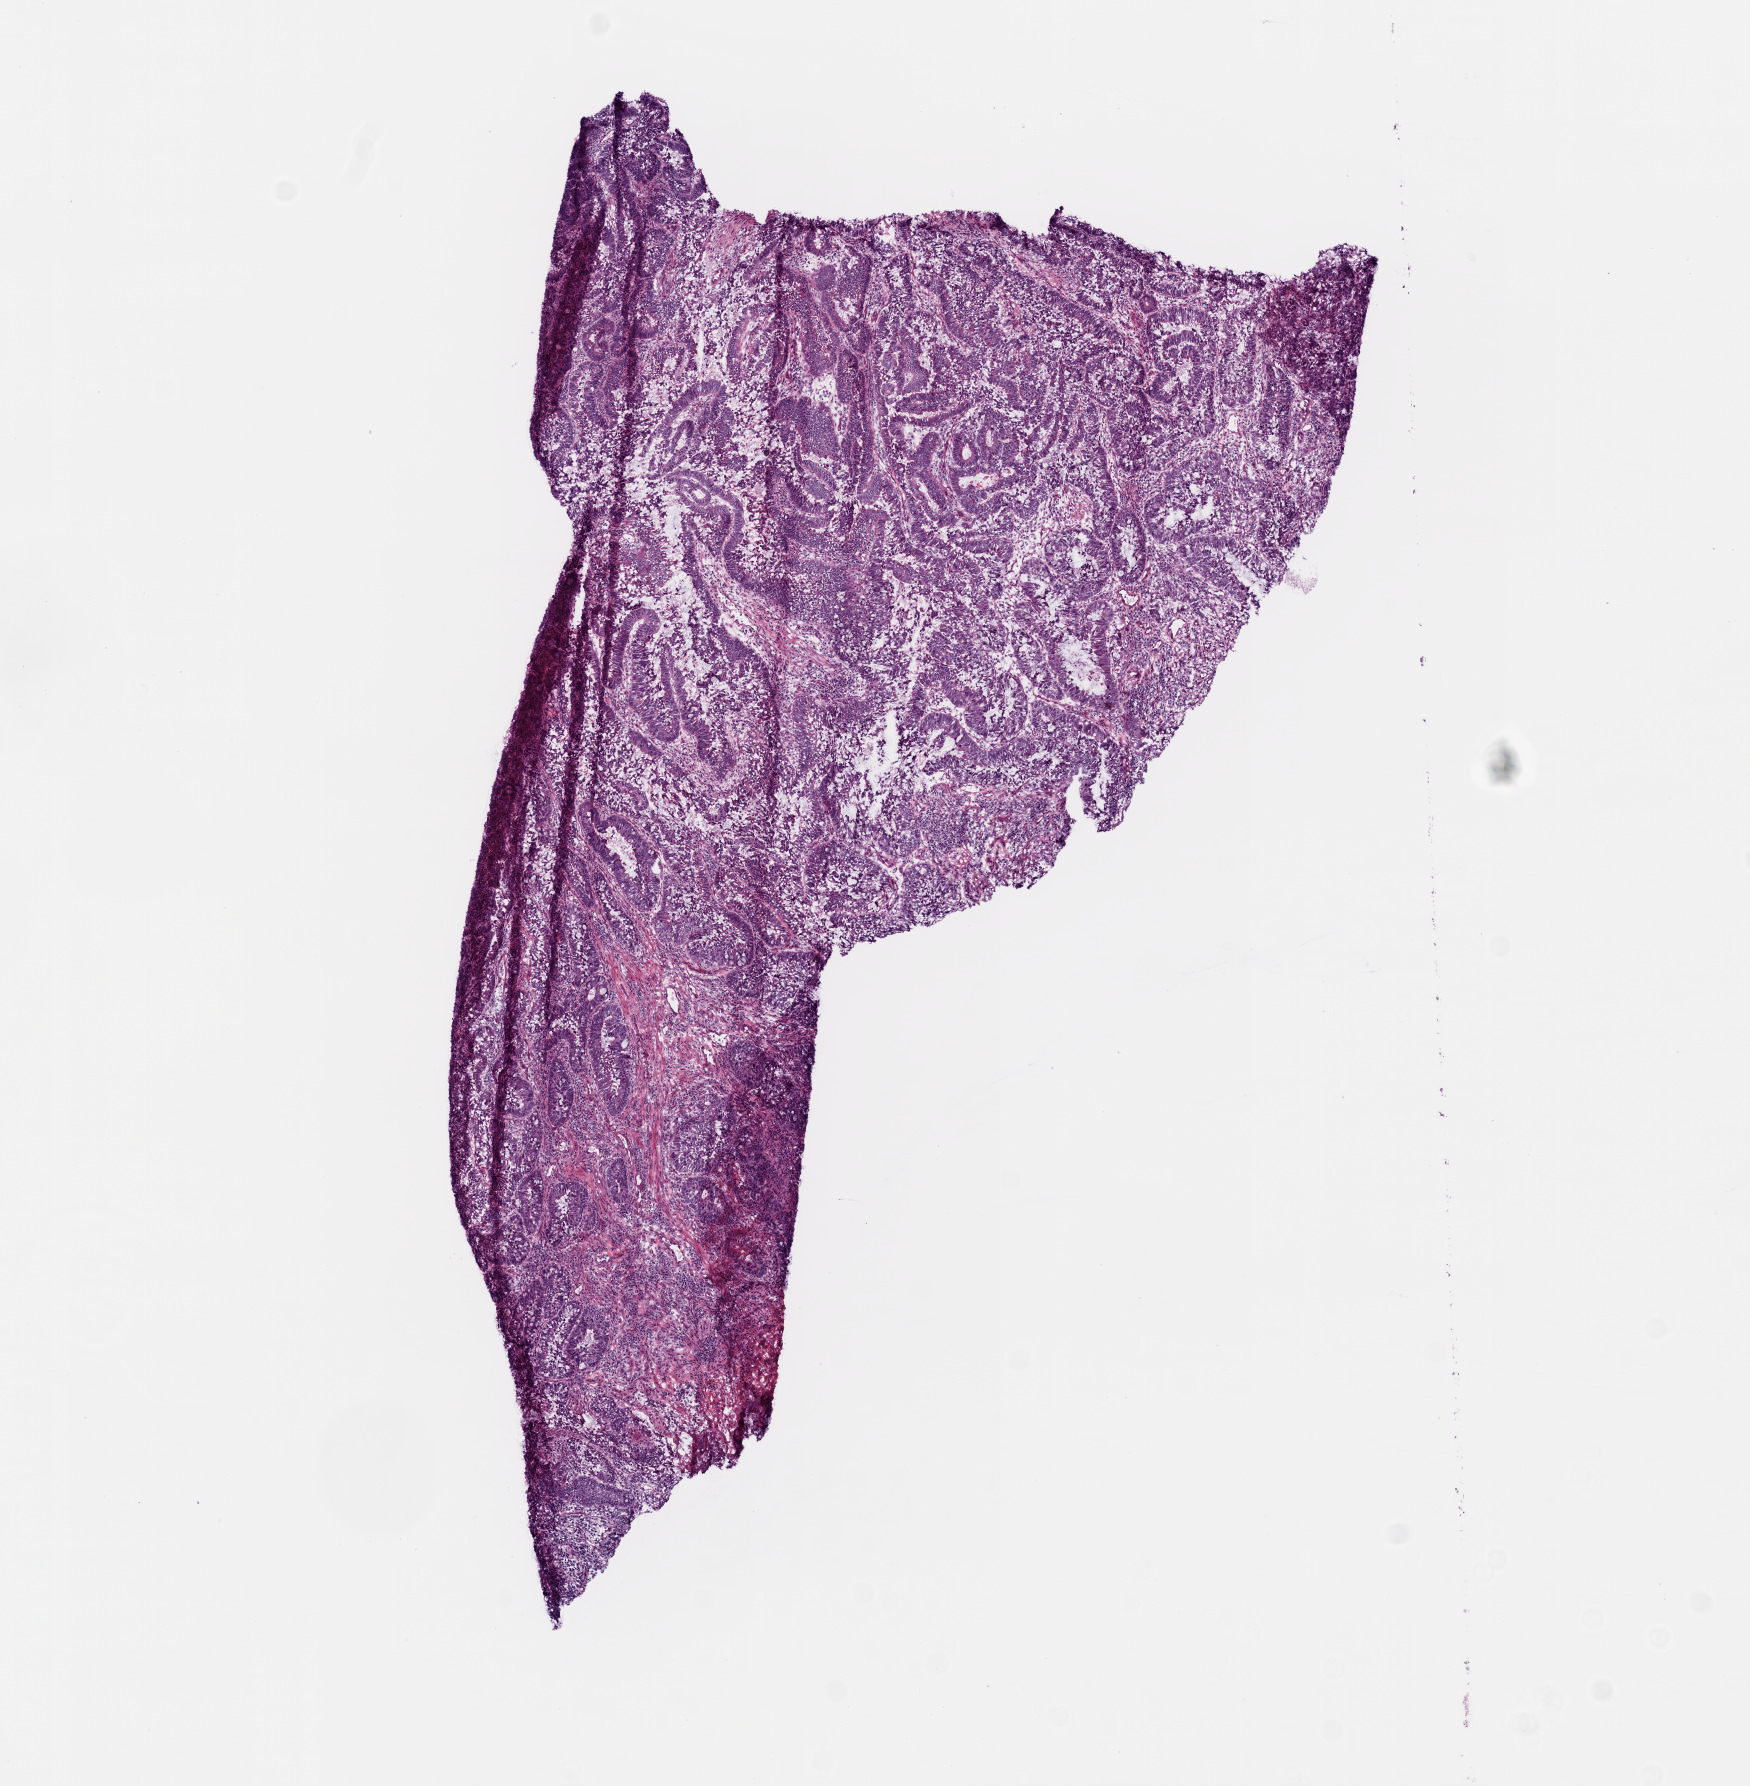
Digitized H&E-stained tissue section (whole slide) — whole scanned area (about 7.0 x 7.2 mm) shown as a low-resolution overview. Frozen section from the top of the tissue portion. Rectum, primary tumour sample. Patient: male, age at initial diagnosis 86 years. Composition of this section per pathologist review: tumour cells 80%, tumour nuclei 75%, normal cells 10%, stromal cells 5%, necrosis 5%.
Lymph nodes positive (case pathology): 5 of 34 examined. TNM: T4 N2 M1. Pathologic diagnosis: Adenocarcinoma, NOS (colon, NOS). AJCC pathologic stage: IV.